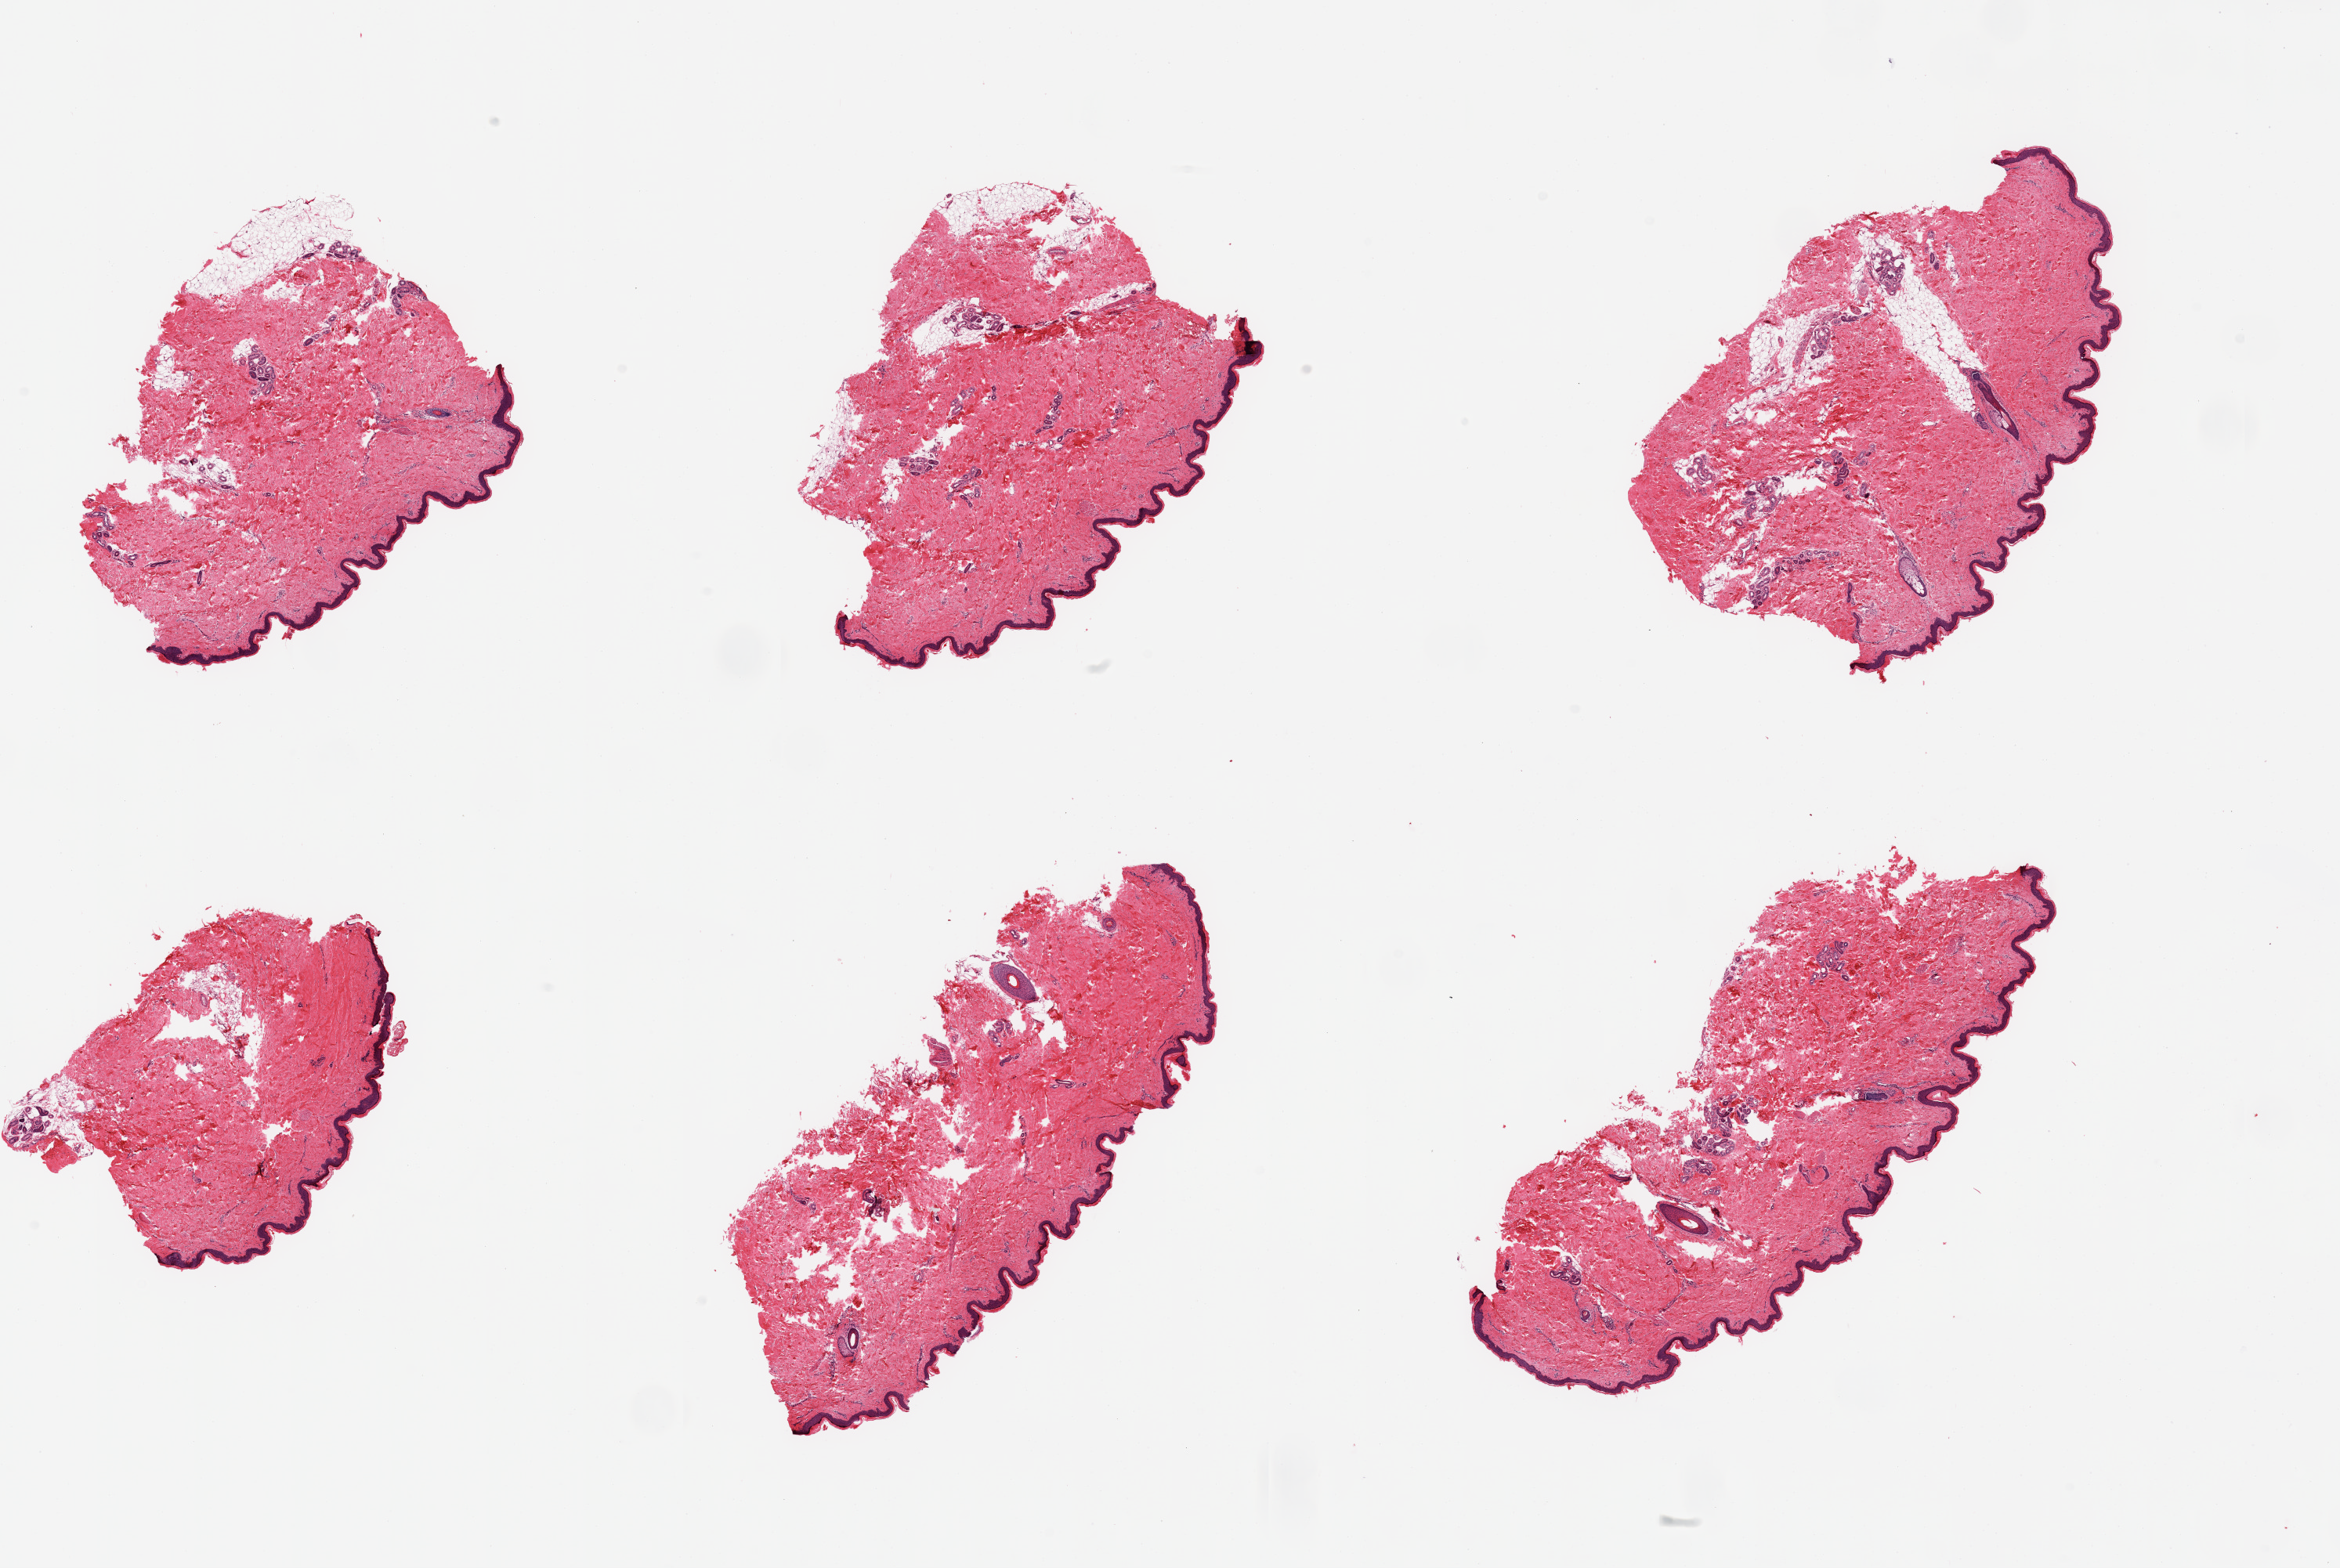
Digitized hematoxylin and eosin (H&E)-stained section — a low-resolution overview of the entire scanned area, about 23.6 x 15.8 mm; PAXgene-fixed, paraffin-embedded tissue; section of skin of lower leg (target tissue); donor tissue sample. Male donor.
- review note (as recorded): 6 pieces, trace dermal fat; squamous epithelium is ~50-60 microns